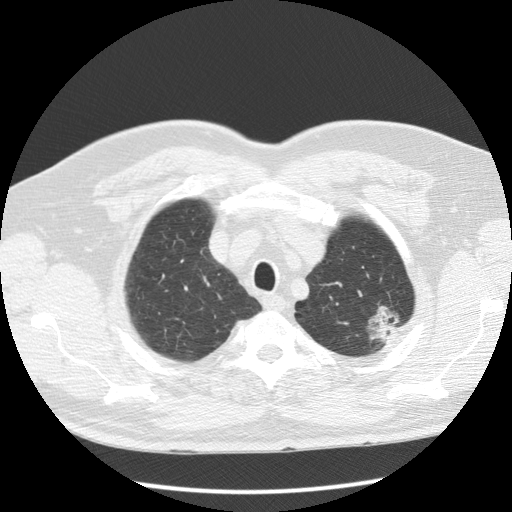
Low-dose screening chest CT, one axial slice; slice 106 of 123 in the series (ordered by position); reconstruction kernel STANDARD; 120 kVp; lung window (W 1500 / L -600 HU); 512 × 512 image matrix.
Annotated regions visible in this slice (manually delineated by an expert):
- lesion 1 (tumor, upper lobe of left lung): bounding box [x1, y1, x2, y2] px = [371, 313, 395, 338]